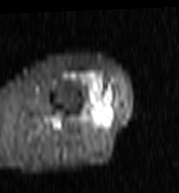
MRI of an extremity soft-tissue mass, one axial slice; position 28 of 103 along the scan axis; STIR; MR volume resampled by the dataset authors to the PET/CT grid (not the native acquisition matrix); 3.27 mm slice thickness; 179 × 193 image matrix. Female patient. Case-level facts recorded for this patient, not image findings: histological type: undifferentiated – high grade; grade: high; site of the primary tumour: left thigh.
Annotated regions visible in this slice (expert contour drawn on MRI and transferred to this co-registered scan by the dataset authors):
- gross tumour volume including surrounding oedema: box from (x=70, y=73) to (x=113, y=116) px